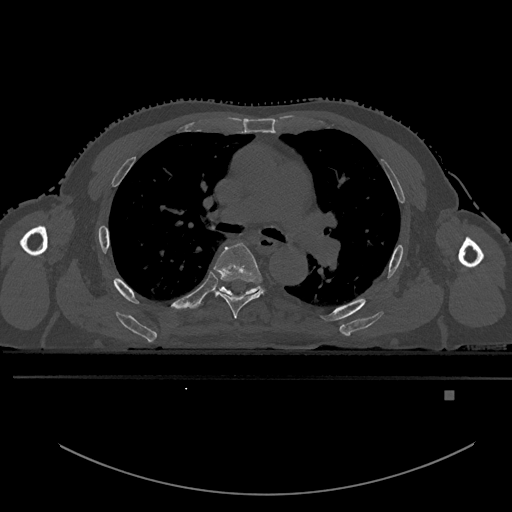
CT including the spine, one axial slice; slice 344 of 969 in the series (ordered by position); bone window (W 1800 / L 400 HU); 512 × 512 image matrix, field of view 456 × 456 mm. Patient: male, 82 years. Case-level facts recorded for this patient, not image findings: primary cancer: prostate; vertebrae with lytic lesions (as recorded): T11, T9, T8, T2.
Structures marked on this image (semi-automatic segmentation, software-assisted and operator-edited):
- T5 vertebra: box from (x=214, y=243) to (x=263, y=319) px
- T6 vertebra: (x=216, y=286)–(x=261, y=297)